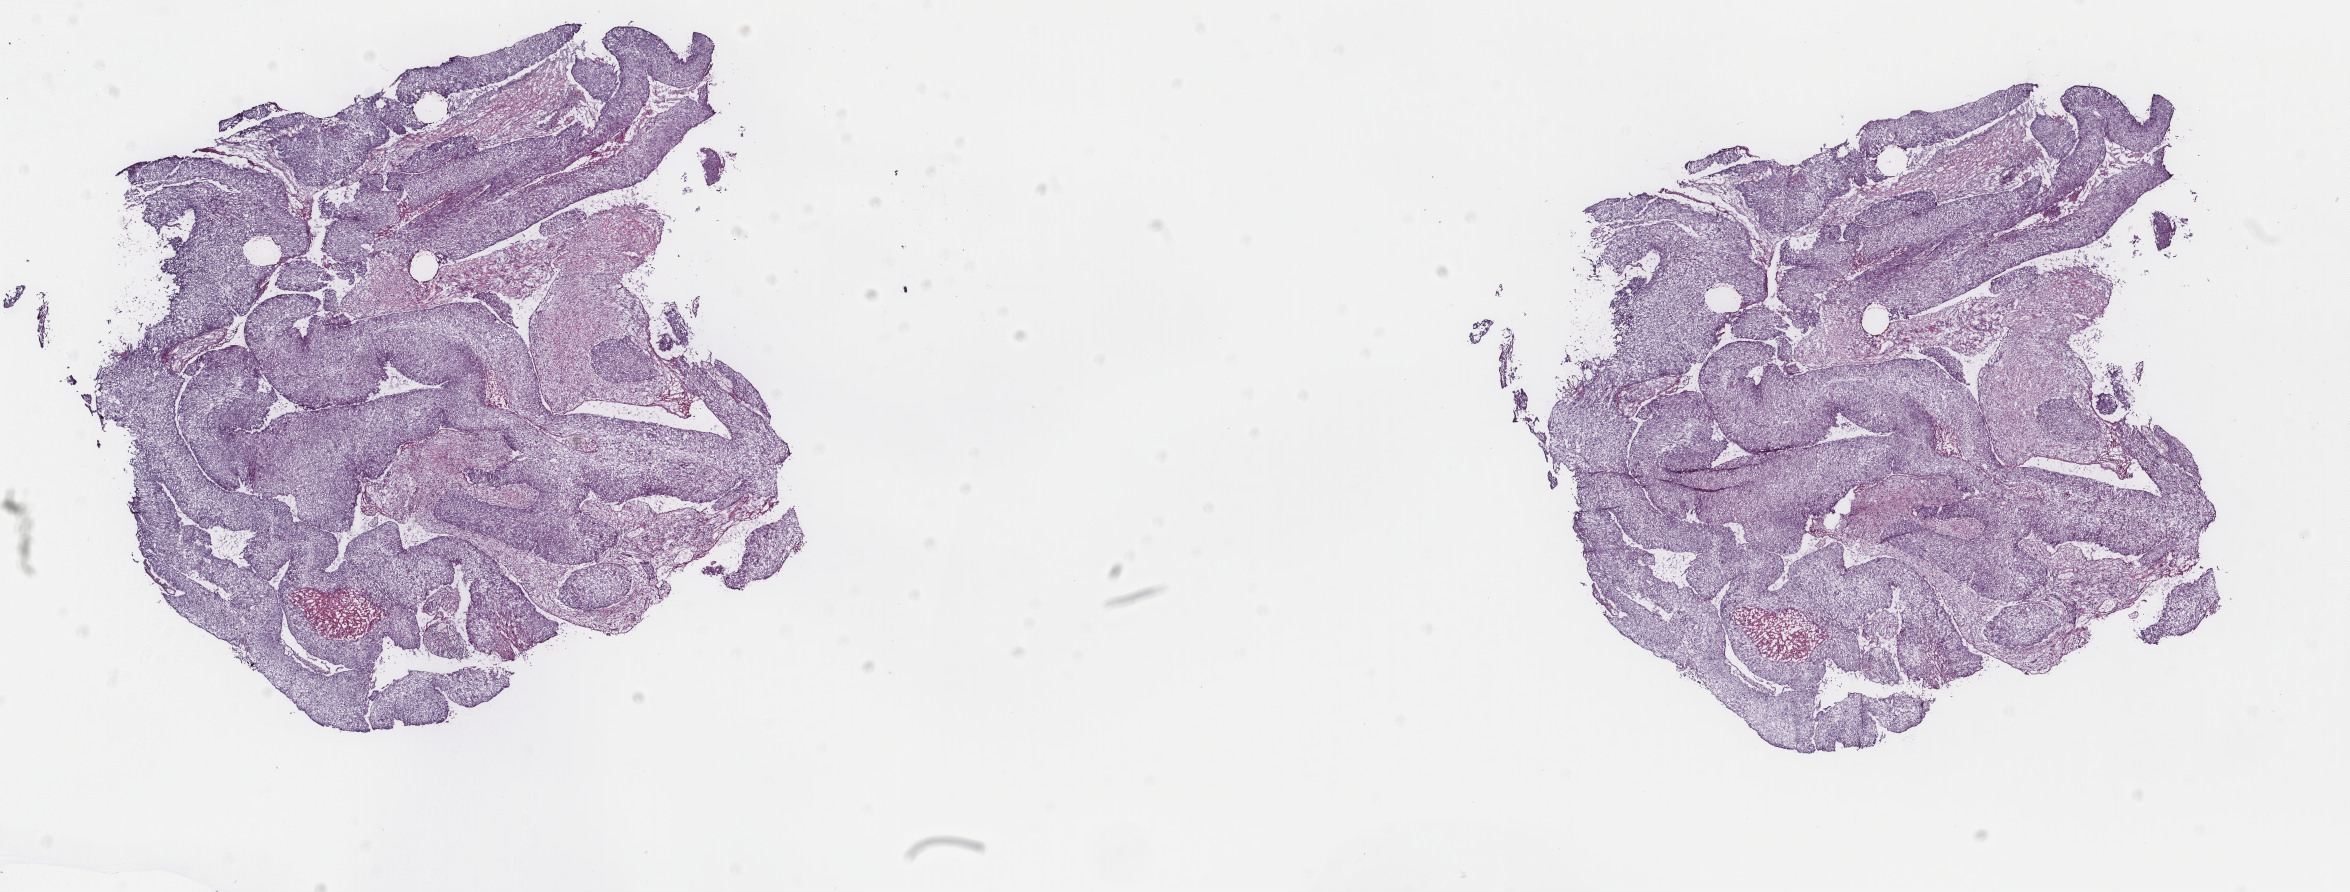
Whole-slide histology image, Hematoxylin and eosin (H&E) stained, shown as a low-resolution overview of the whole scanned area (about 18.7 x 7.1 mm, acquisition: 40x scan); frozen section from the top of the tissue portion; sample: primary tumour, bladder. Male, age 75 years at initial diagnosis. Pathologist review of this section (percent, as recorded): tumour cells 95%, tumour nuclei 95%.
Pathologic diagnosis: Transitional cell carcinoma.